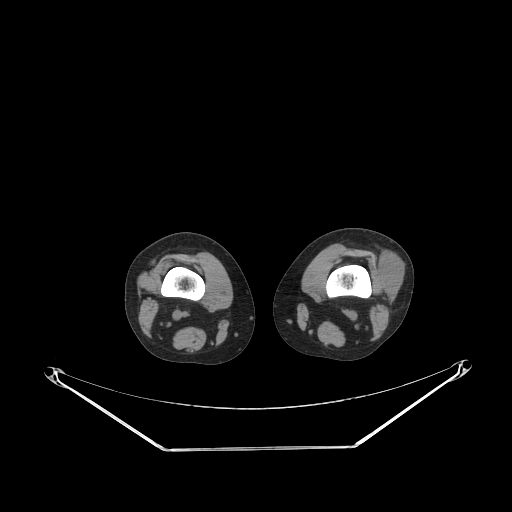
CT of an extremity soft-tissue mass (from a PET/CT study), one axial slice; slice 173 of 223 in the series (ordered by position); 140 kVp; soft-tissue window (W 400 / L 40 HU); 512 × 512 image matrix, field of view 500 × 500 mm. Female patient. From the clinical record (not read from this slice): histological type: spindle cell suggestive of biphasic synovial sarcoma; grade: intermediate; site of the primary tumour: left knee.
Annotated regions visible in this slice (expert contour drawn on MRI and transferred to this co-registered scan by the dataset authors):
- gross tumour volume including surrounding oedema: bounding box [x1, y1, x2, y2] px = [372, 249, 401, 298]
- gross tumour volume (mass): [374, 251, 401, 298]